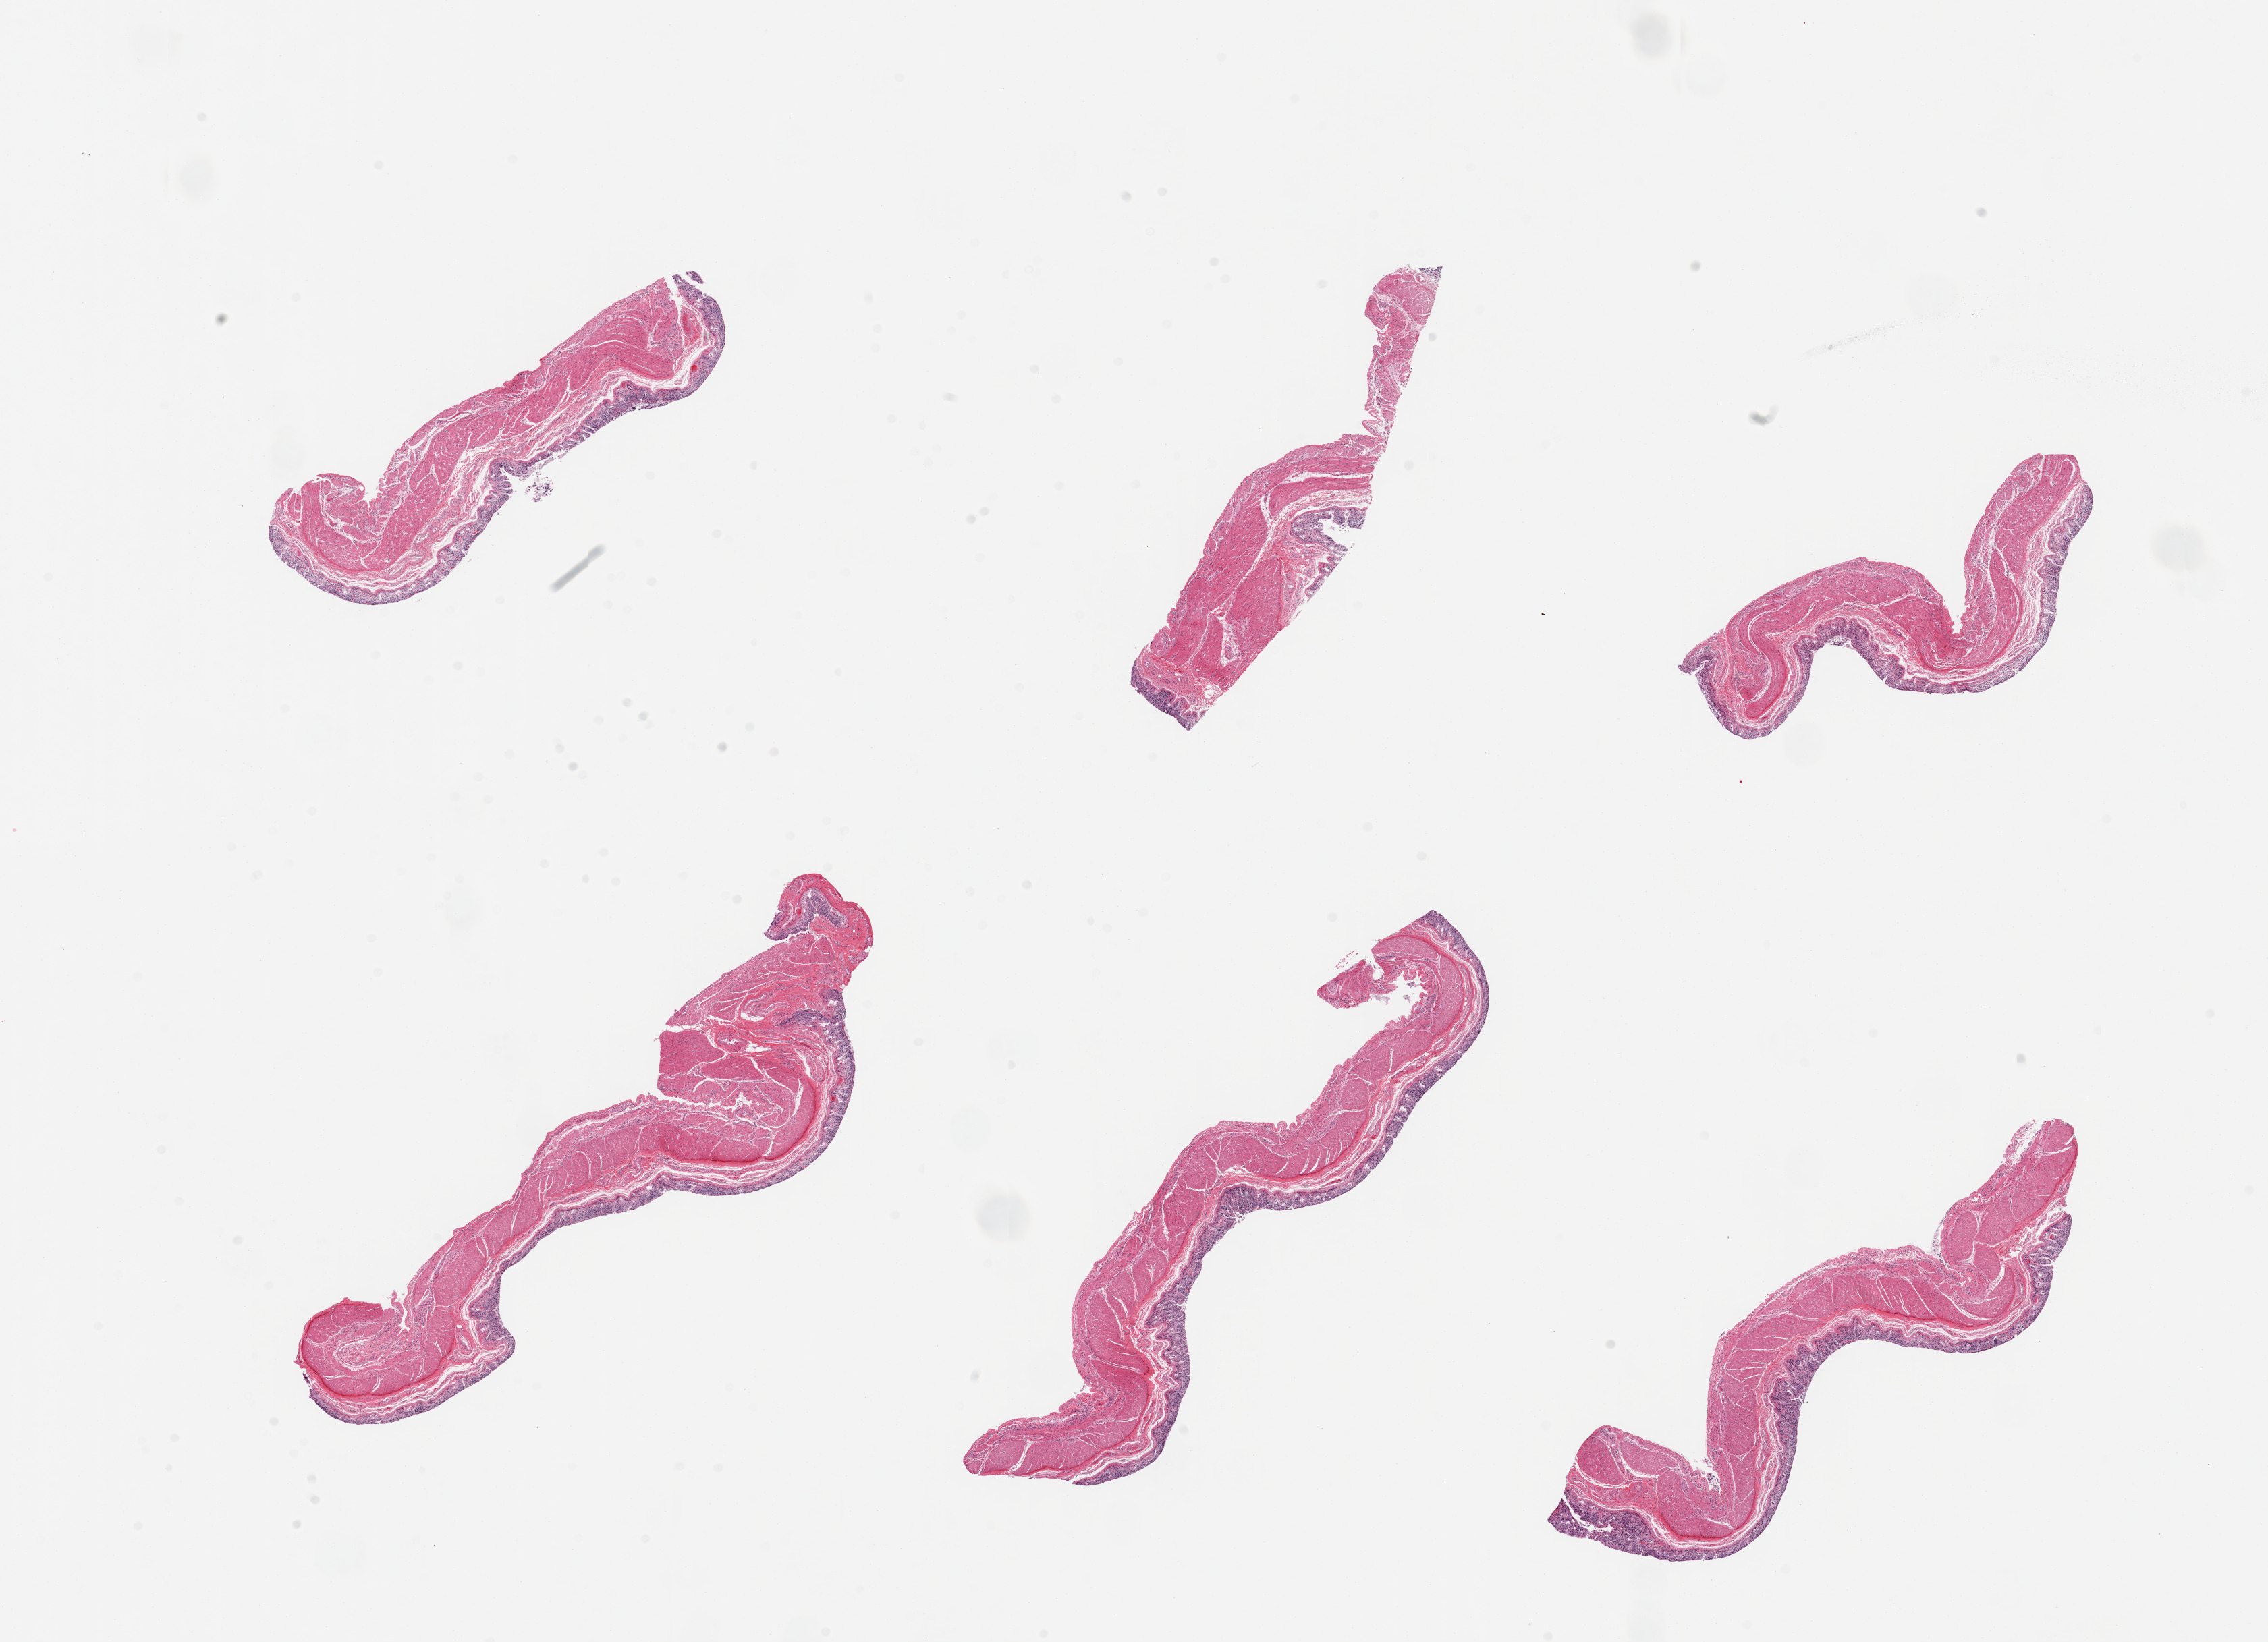
Whole-slide image, H&E stain, shown as a low-resolution overview of the whole scanned area (about 26.6 x 19.2 mm, slide scanned at 20x). PAXgene-fixed, paraffin-embedded tissue. Section of transverse colon (target tissue). Tissue donor sample. Donor: male.
- review note (as recorded): 6 pieces; full thickness sections, mucosa moderately to severely auytolyzed